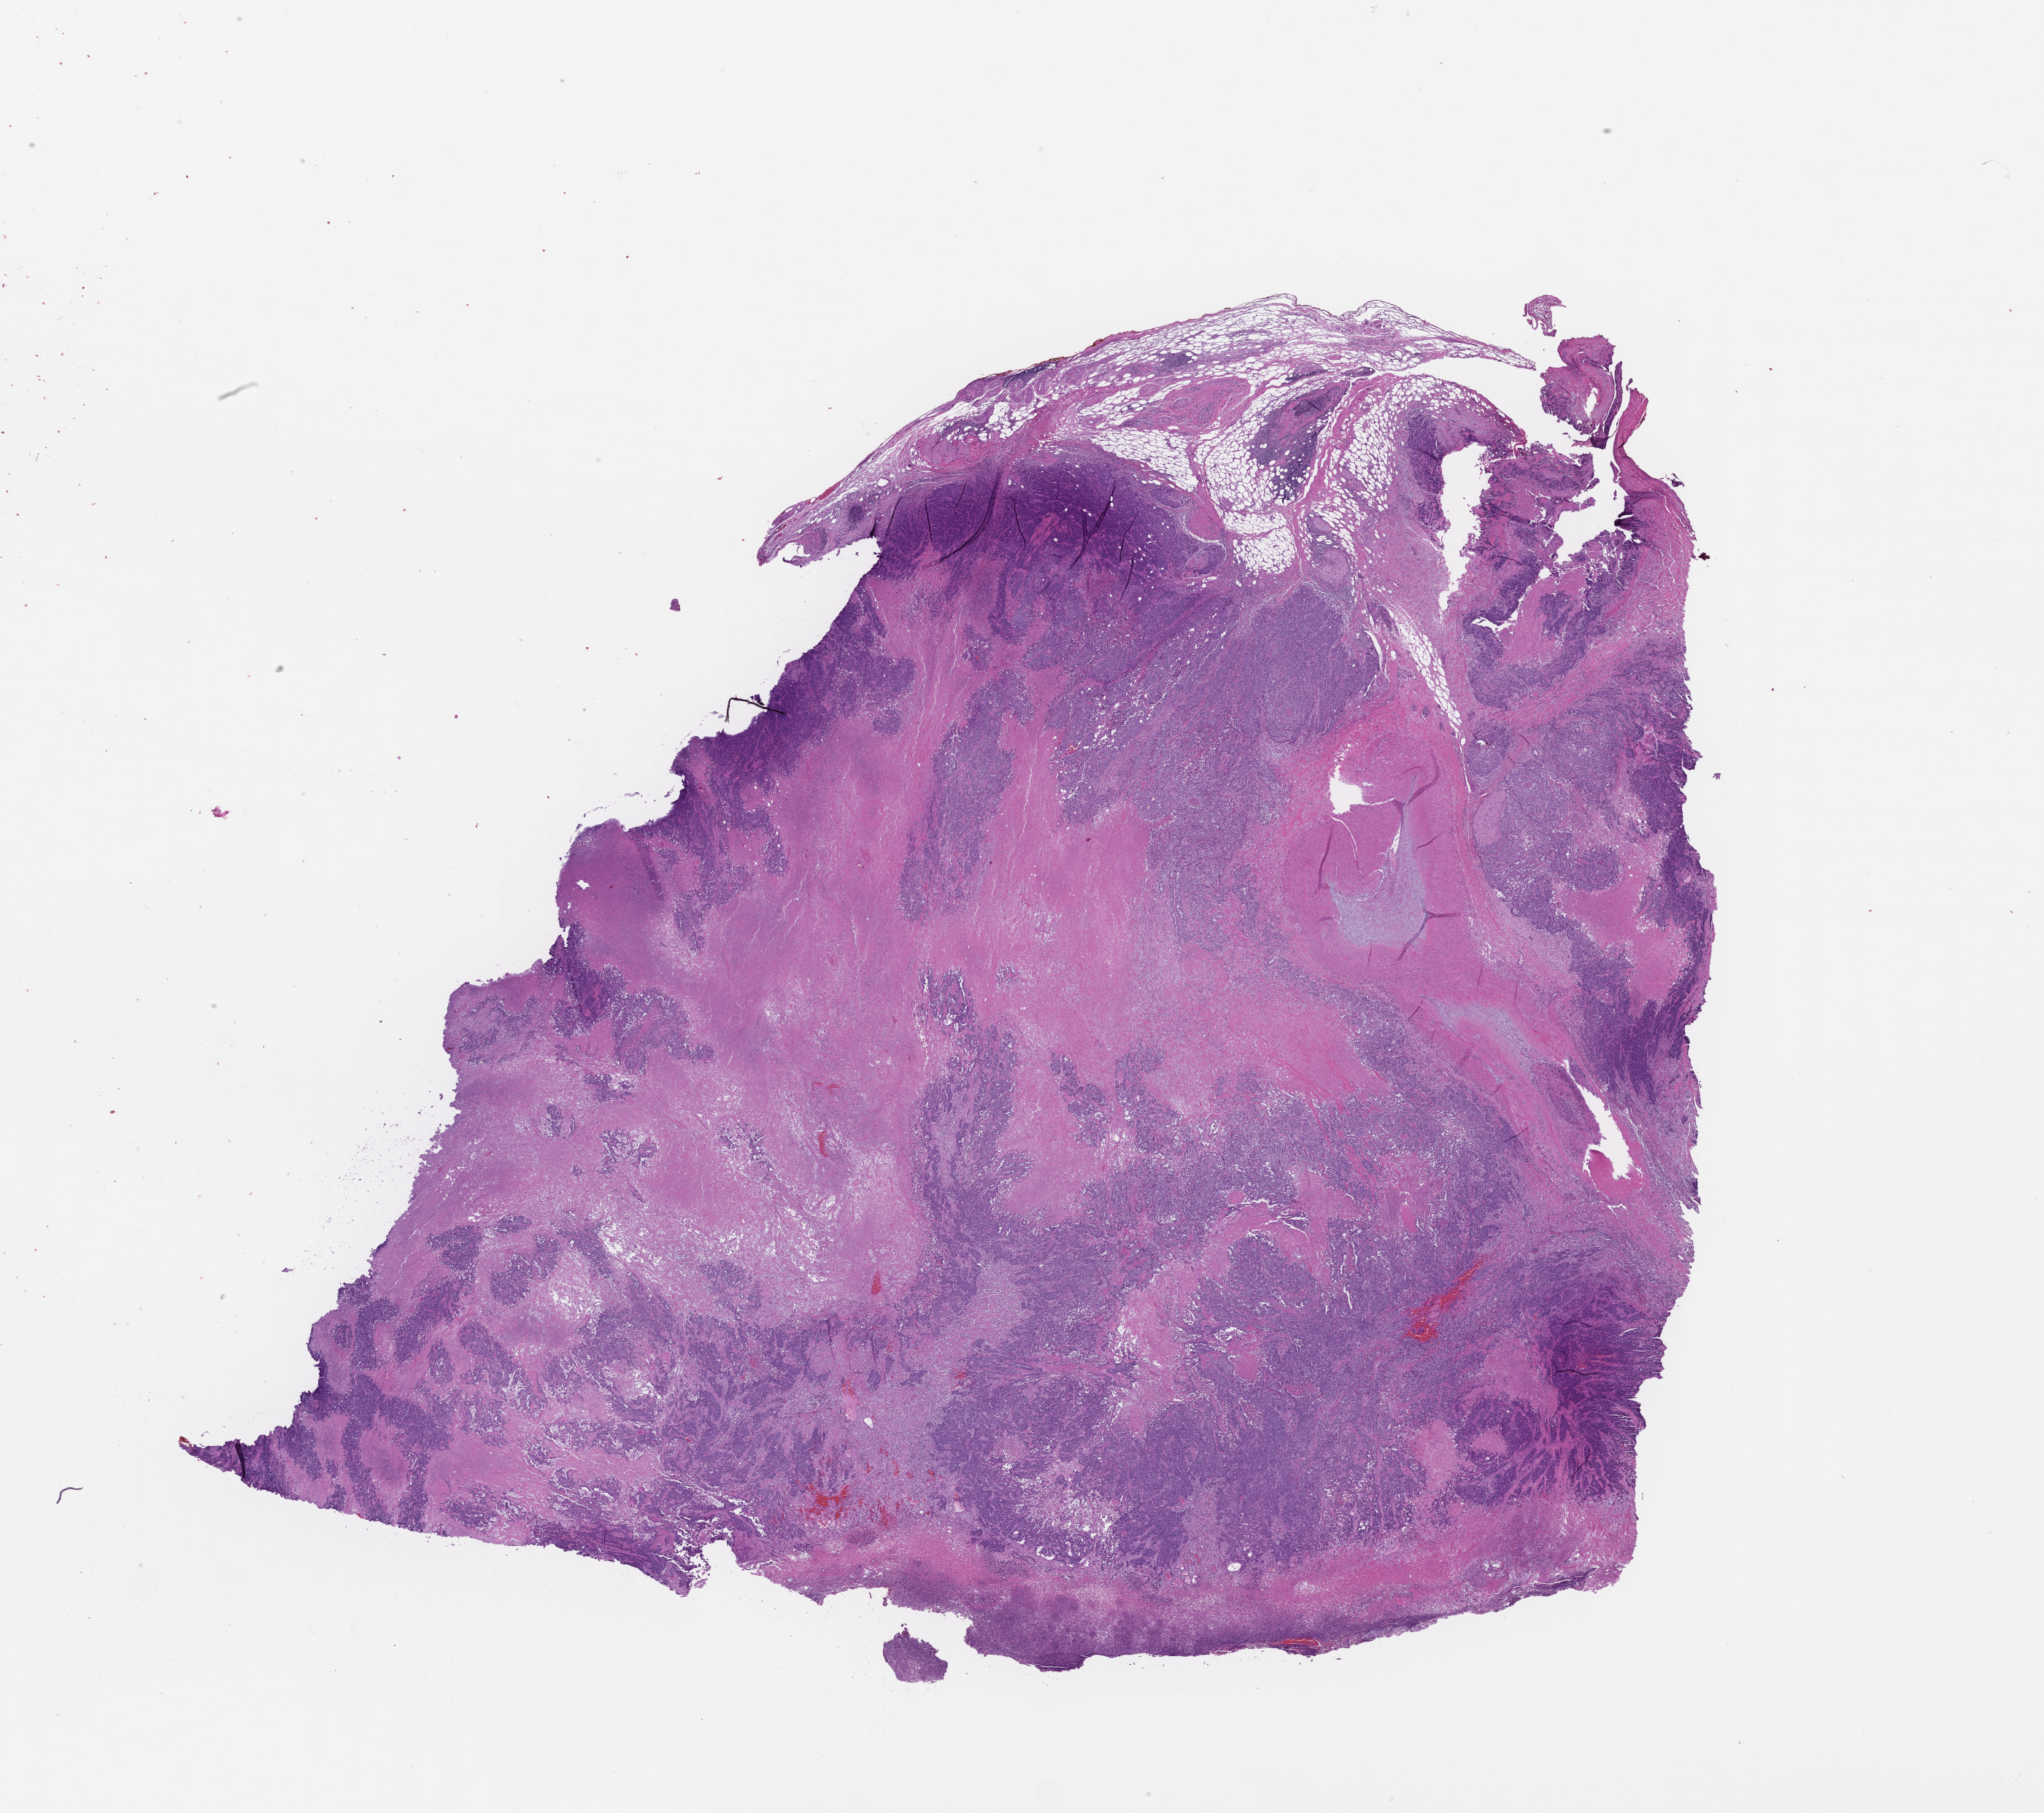
Whole-slide image, H&E stain — whole scanned area (about 22.6 x 20.1 mm) shown as a low-resolution overview. FFPE section. Site: colon. Specimen time point: archival tissue. Patient: male.
• this section: primary tumor
• diagnosis: Colorectal Carcinoma